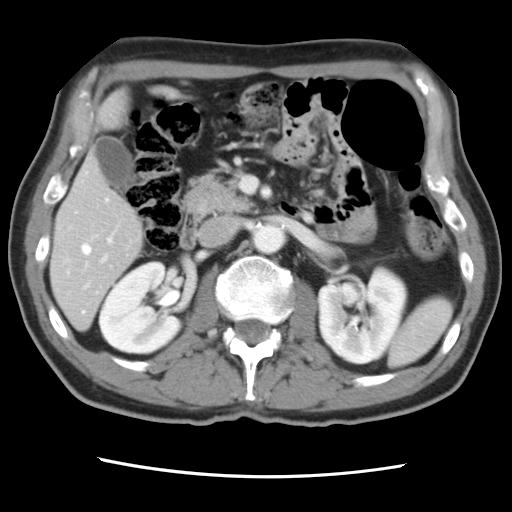
Contrast-enhanced abdominal CT, one axial slice. Slice 37 of 83 in the series (ordered by position). 120 kVp. Intravenous contrast given. Soft-tissue window (W 400 / L 40 HU). 5 mm slice thickness. 512 × 512 image matrix, field of view 321 × 321 mm. Male patient, age 69 years. From the clinical record (not read from this slice): diagnosis: colorectal cancer liver metastases, imaged before liver resection.
Annotated regions visible in this slice (manually delineated by an expert):
- hepatic veins: bounding box (x1, y1, x2, y2) in pixels: (82, 199, 109, 312)
- liver: (52, 95, 144, 328)
- planned liver remnant (the part of the liver to remain after resection): (52, 158, 144, 328)
- portal vein (with intrahepatic branches): (83, 226, 118, 289)